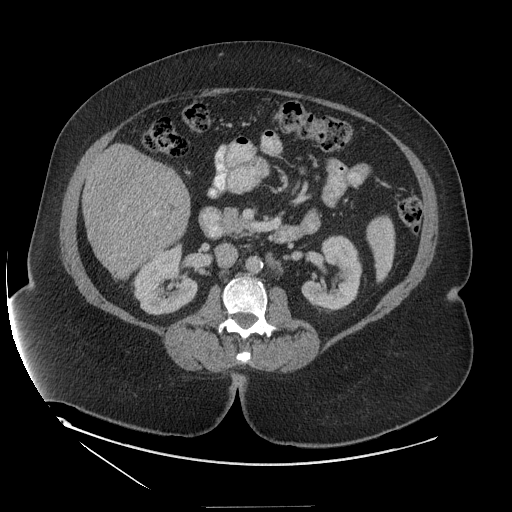
Contrast-enhanced abdominal CT (liver protocol), one axial slice. 140 kVp. Soft-tissue window (W 400 / L 40 HU). 2.5 mm slice thickness. 512 × 512 image matrix, field of view 480 × 480 mm. Case-level facts recorded for this patient, not image findings: diagnosis: hepatocellular carcinoma (patient treated with transarterial chemoembolisation; whether this scan precedes or follows treatment is not stated here); TNM stage (as recorded): Stage-II; Child-Pugh class: A; tumour differentiation: well differentiated.
Annotated regions visible in this slice (semi-automatically segmented with operator editing):
- liver parenchyma outside the tumour (the mass and vessels are separate outlines, so this box may not span the whole liver): bounding box (x1, y1, x2, y2) in pixels: (82, 144, 190, 277)